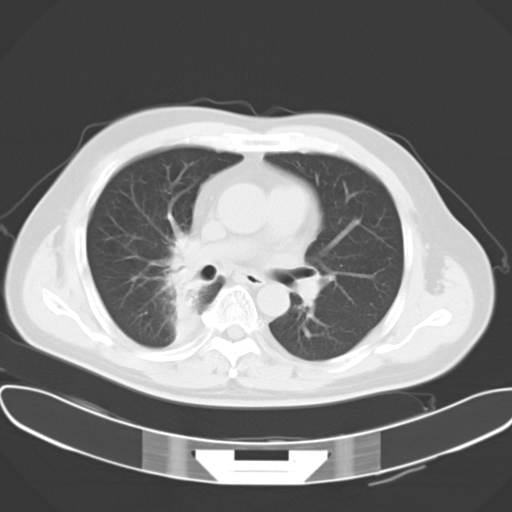
Chest CT, one axial slice; position 16 of 28 along the scan axis; 120 kVp; lung window (W 1500 / L -600 HU); 10 mm slice thickness; 512 × 512 image matrix, field of view 388 × 388 mm. Patient: male, 48 years. From the clinical record (not read from this slice): clinical TNM (as recorded): T1a N1 M1c; histopathological grade: G3.
Annotated regions visible in this slice (rectangle marked by the reading radiologist):
- lung tumour (recorded histology: adenocarcinoma): box from (x=166, y=236) to (x=219, y=312) px